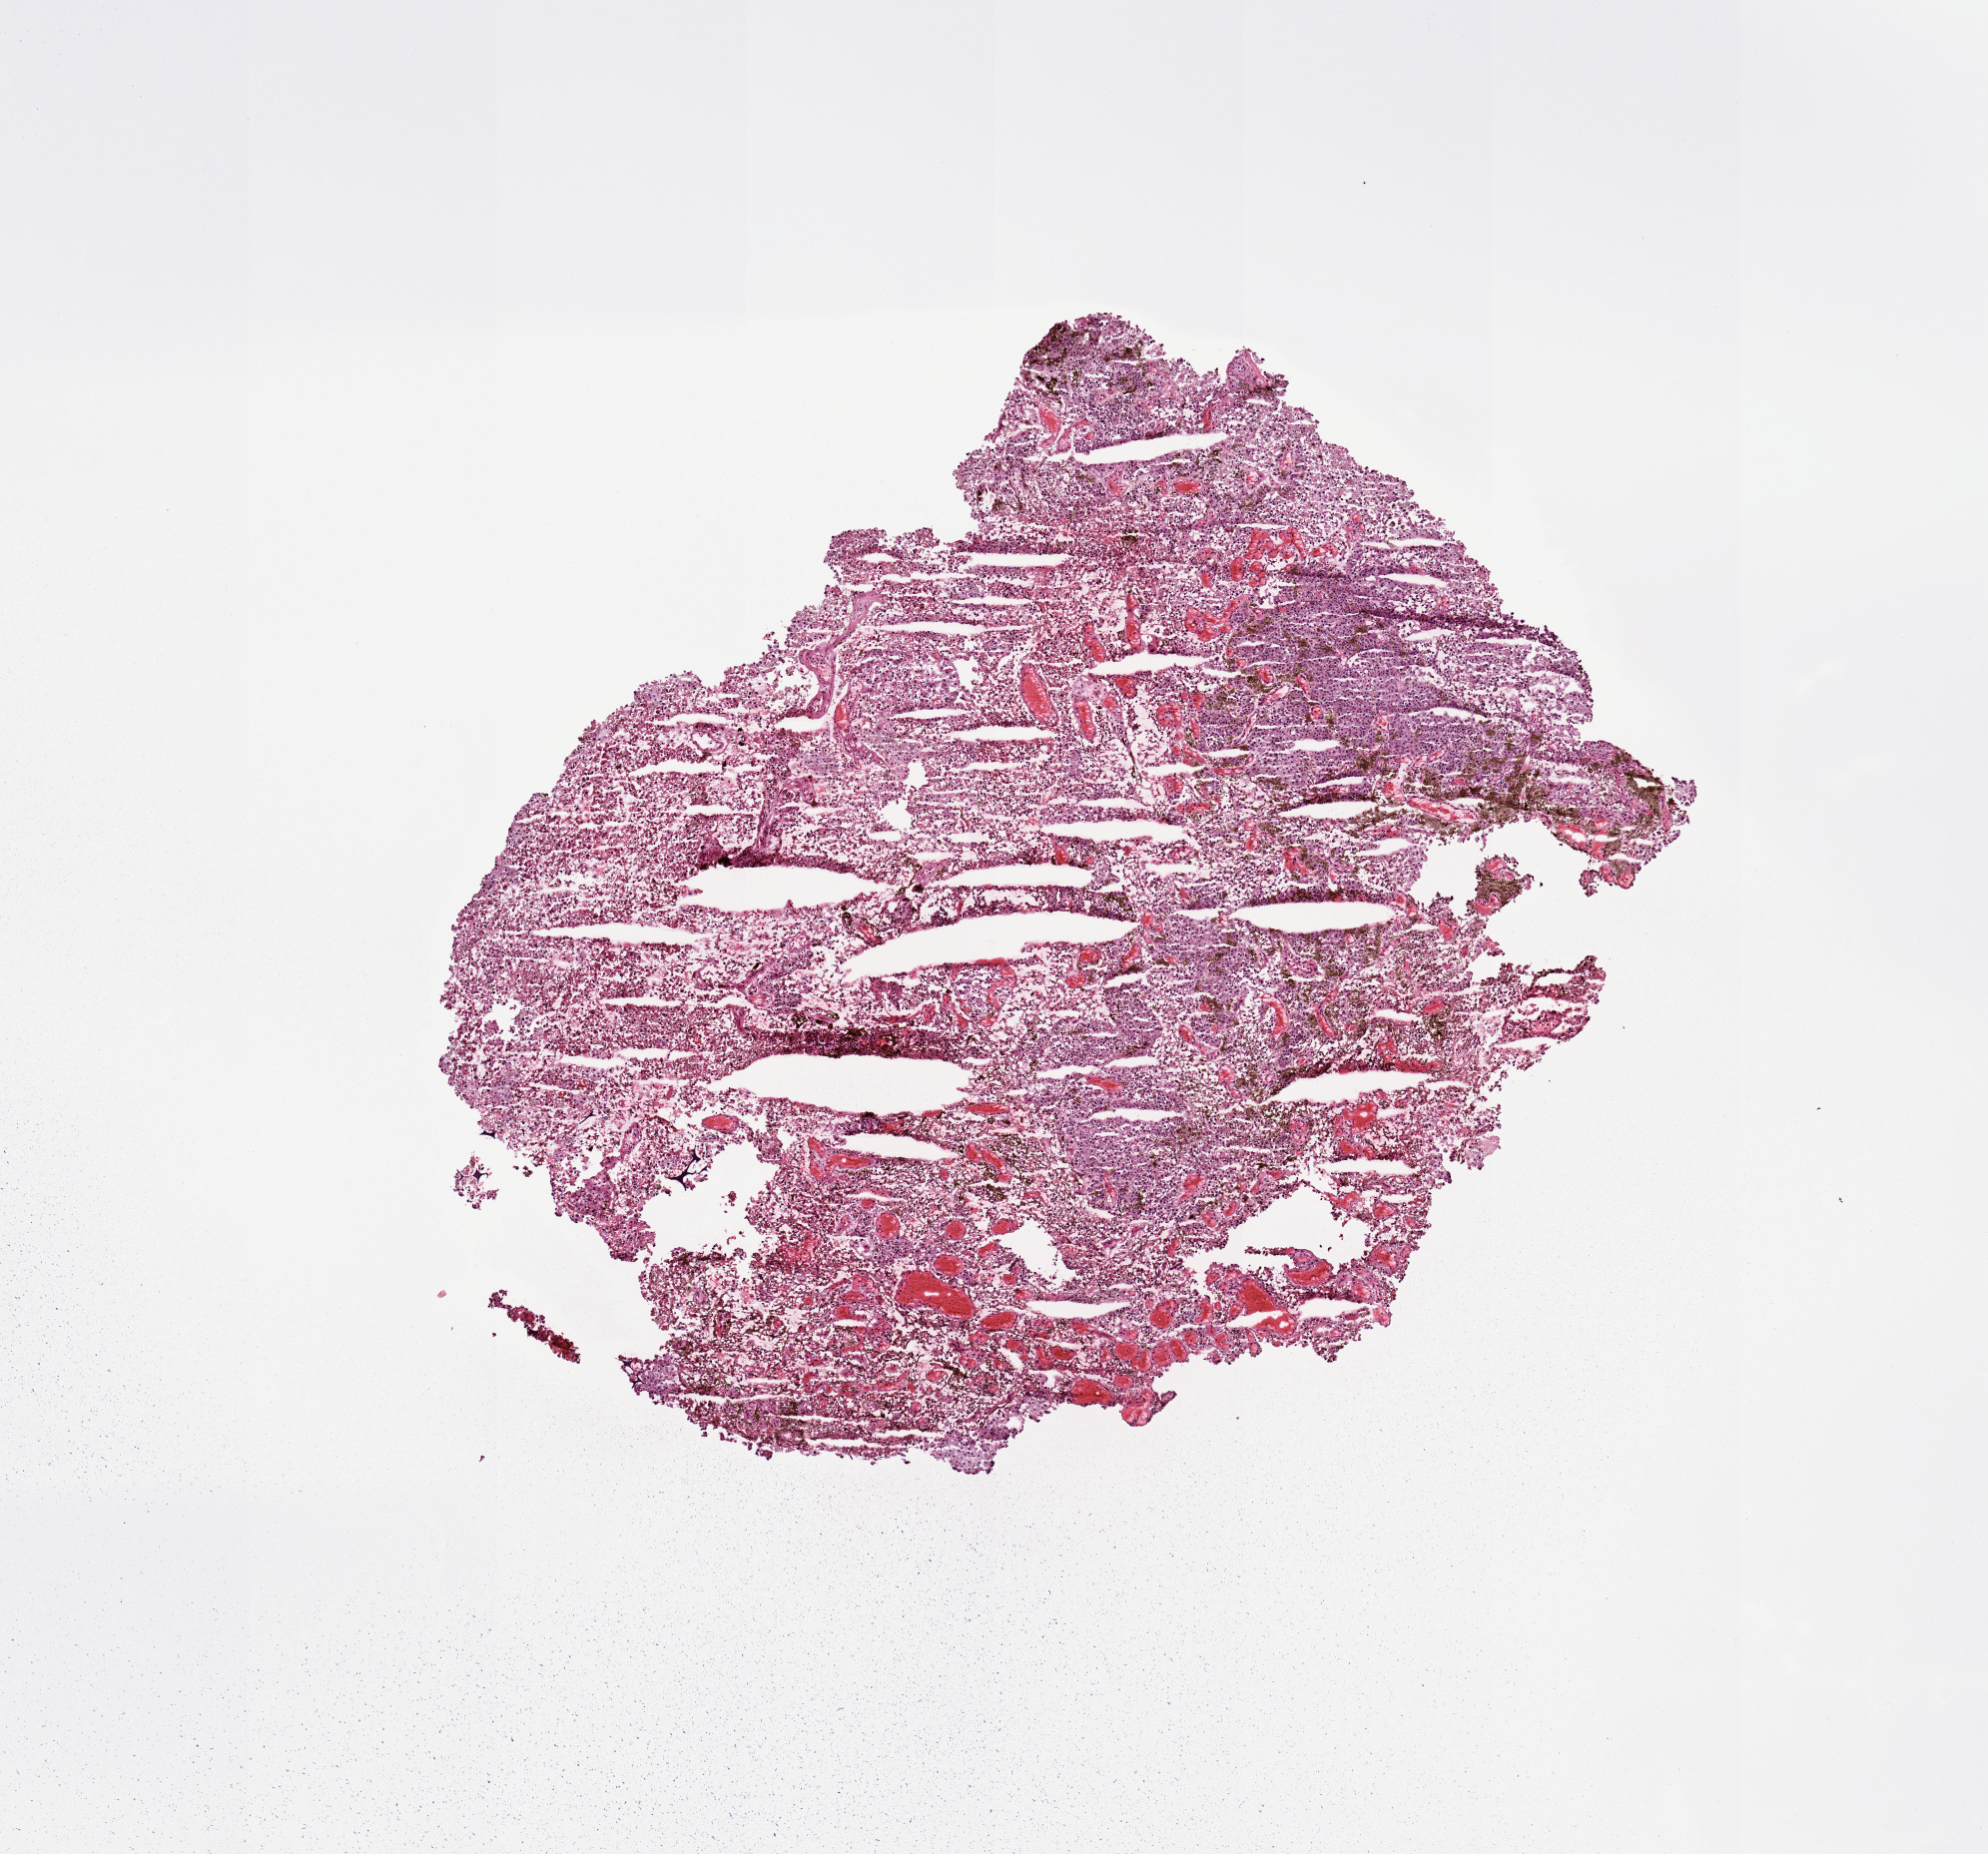
Whole-slide histology image, H&E-stained — low-resolution overview of the scanned area, about 7.9 x 7.3 mm, melanoma tumour tissue; sampled site not recorded. Male, 75 y/o.
Primary tumour site (as recorded): head & neck. Patient diagnosis (cohort enrolment): cutaneous melanoma (skin).